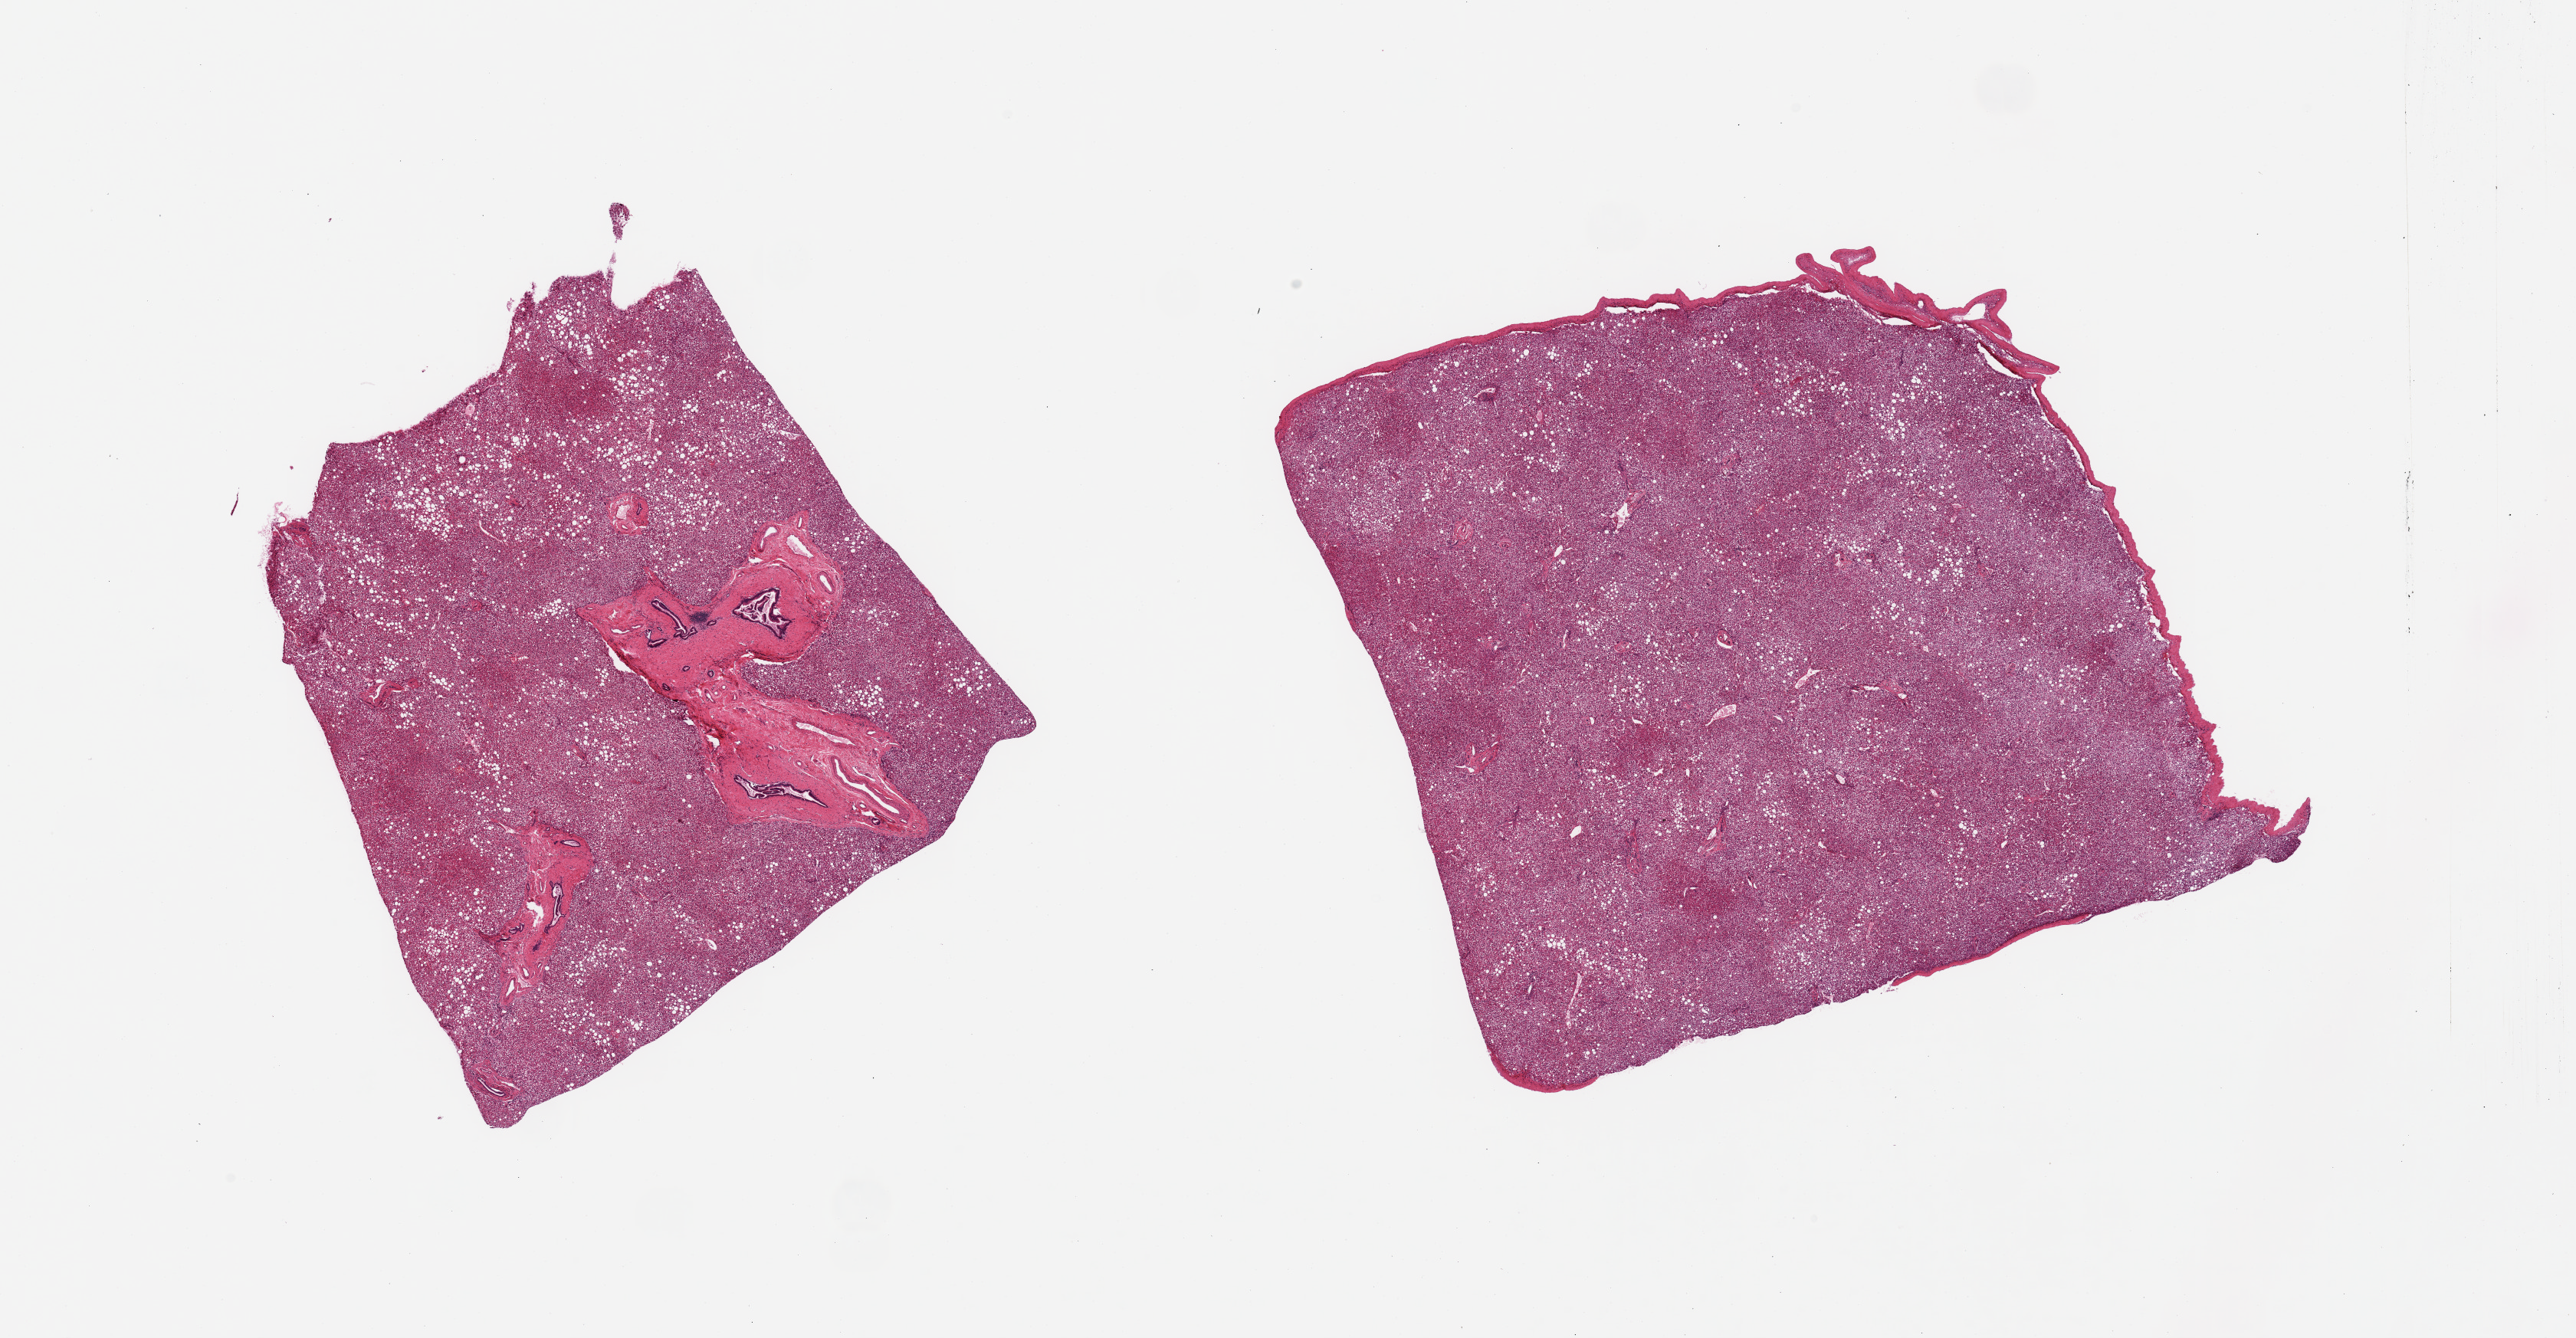
Digitized H&E-stained section — a low-resolution overview of the entire scanned area, about 26.6 x 13.8 mm (slide scanned at 20x). PAXgene-fixed paraffin-embedded (PFPE) section. Sampled site (target tissue): liver. Donor tissue sample. Donor: female.
Review note (as recorded): 2 pieces; diffuse fatty degeneration (large and small fat droplets); one with bile ducts surrounded by dense fibrous tissue and other covered by capsule at two sides.